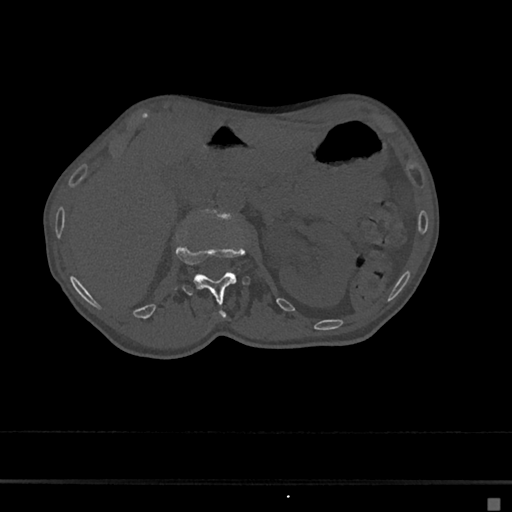
CT including the spine, one axial slice. Bone window (W 1800 / L 400 HU). 0.5 mm slice thickness. 512 × 512 image matrix, field of view 360 × 360 mm. Patient: female, 68 years. From the clinical record (not read from this slice): primary cancer: renal.
Structures marked on this image (semi-automatic segmentation, software-assisted and operator-edited):
- L1 vertebra: bounding box <173,241,251,317> (left, top, right, bottom; pixels)
- L2 vertebra: <208,211,219,215>